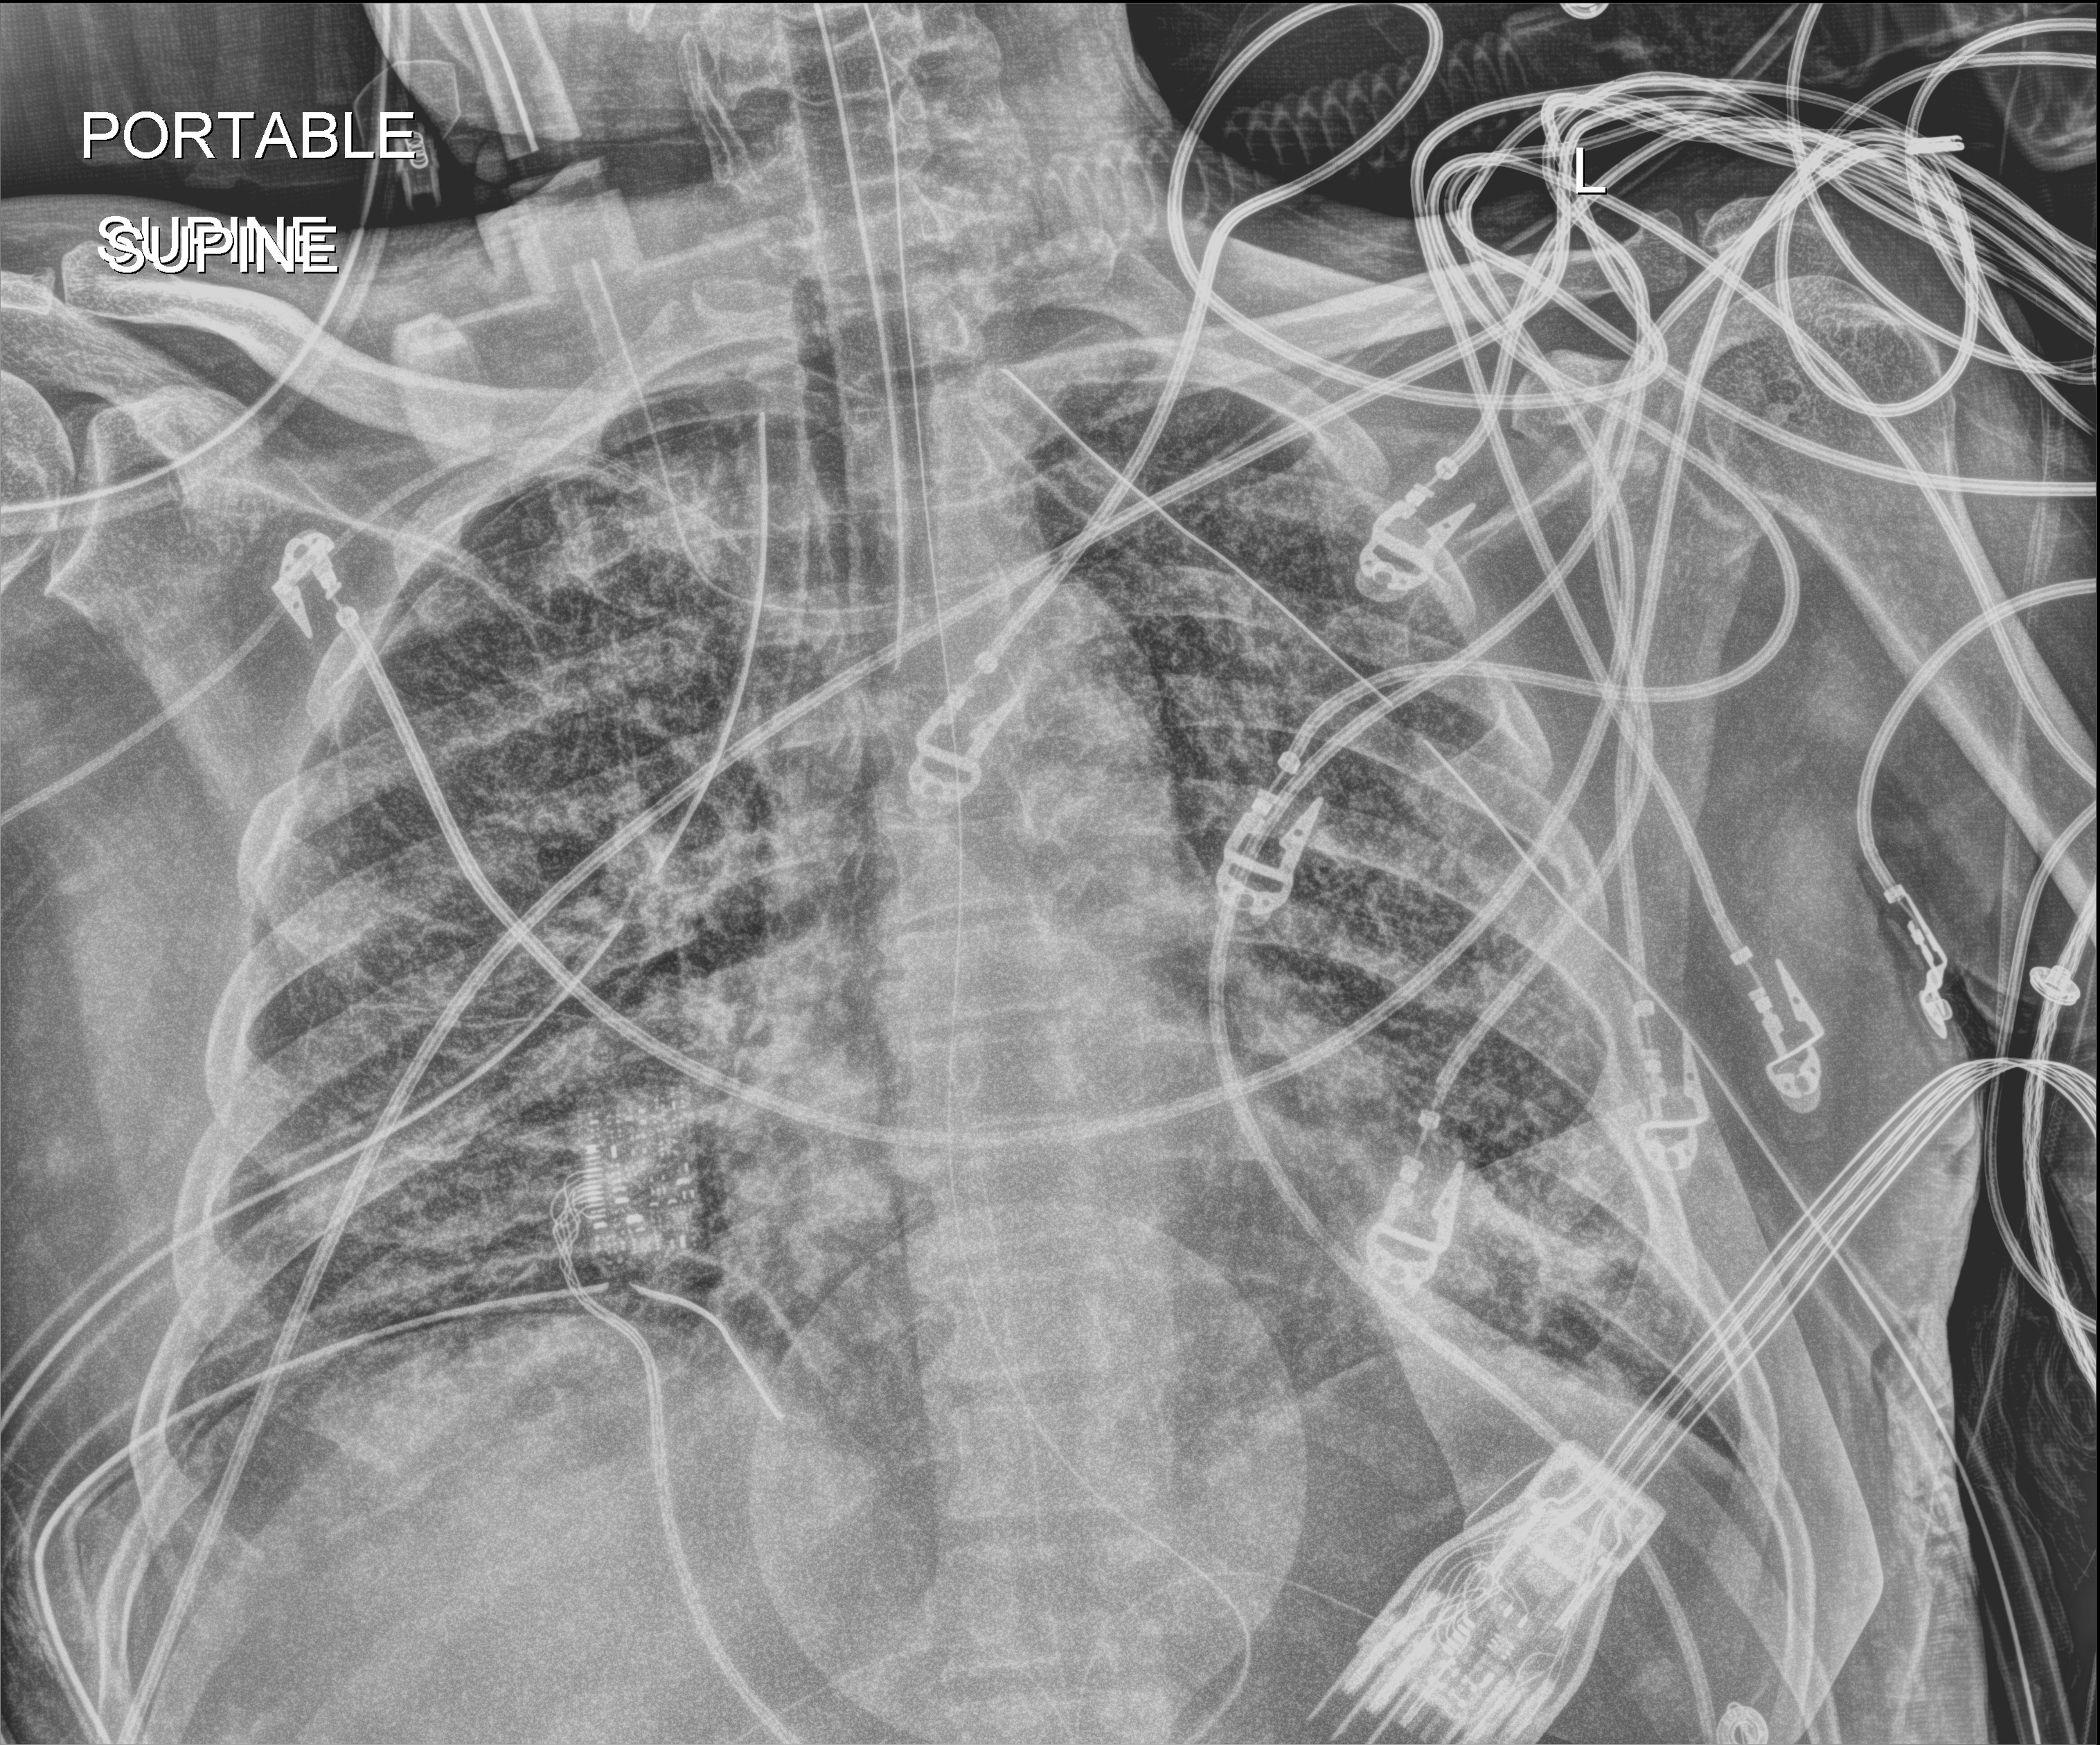
Bedside chest radiograph (digital radiography), anteroposterior (AP) projection. Male patient hospitalised with COVID-19, age 18–59 years.
Admission-level facts for this patient (not findings on this image; timing relative to this image not recorded): hypertension (admission record): yes; admitted to intensive care during this hospital stay: yes; mechanically ventilated during this hospital stay: yes.